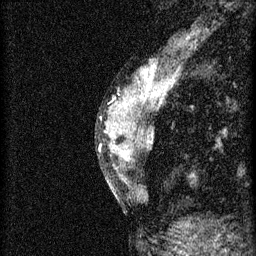
Breast MRI (dynamic contrast-enhanced), one sagittal slice; slice 21 of 46 in the series (ordered by position); 3 images stored at this slice position (order not interpretable as contrast timing); 1.5 T; TE 4.2 ms, TR 8.2 ms; 256 × 256 image matrix, field of view 180 × 180 mm. Patient: female, 44 years.
Structures marked on this image (semi-automatic segmentation, software-assisted and operator-edited):
- analysis volume of interest (the breast-tissue region the enhancement analysis was run in; not a lesion): bounding box [x1, y1, x2, y2] px = [110, 128, 153, 181]
- tumour enhancement mask (voxels above the 70 % enhancement threshold inside the analysis volume of interest): [114, 136, 129, 159]